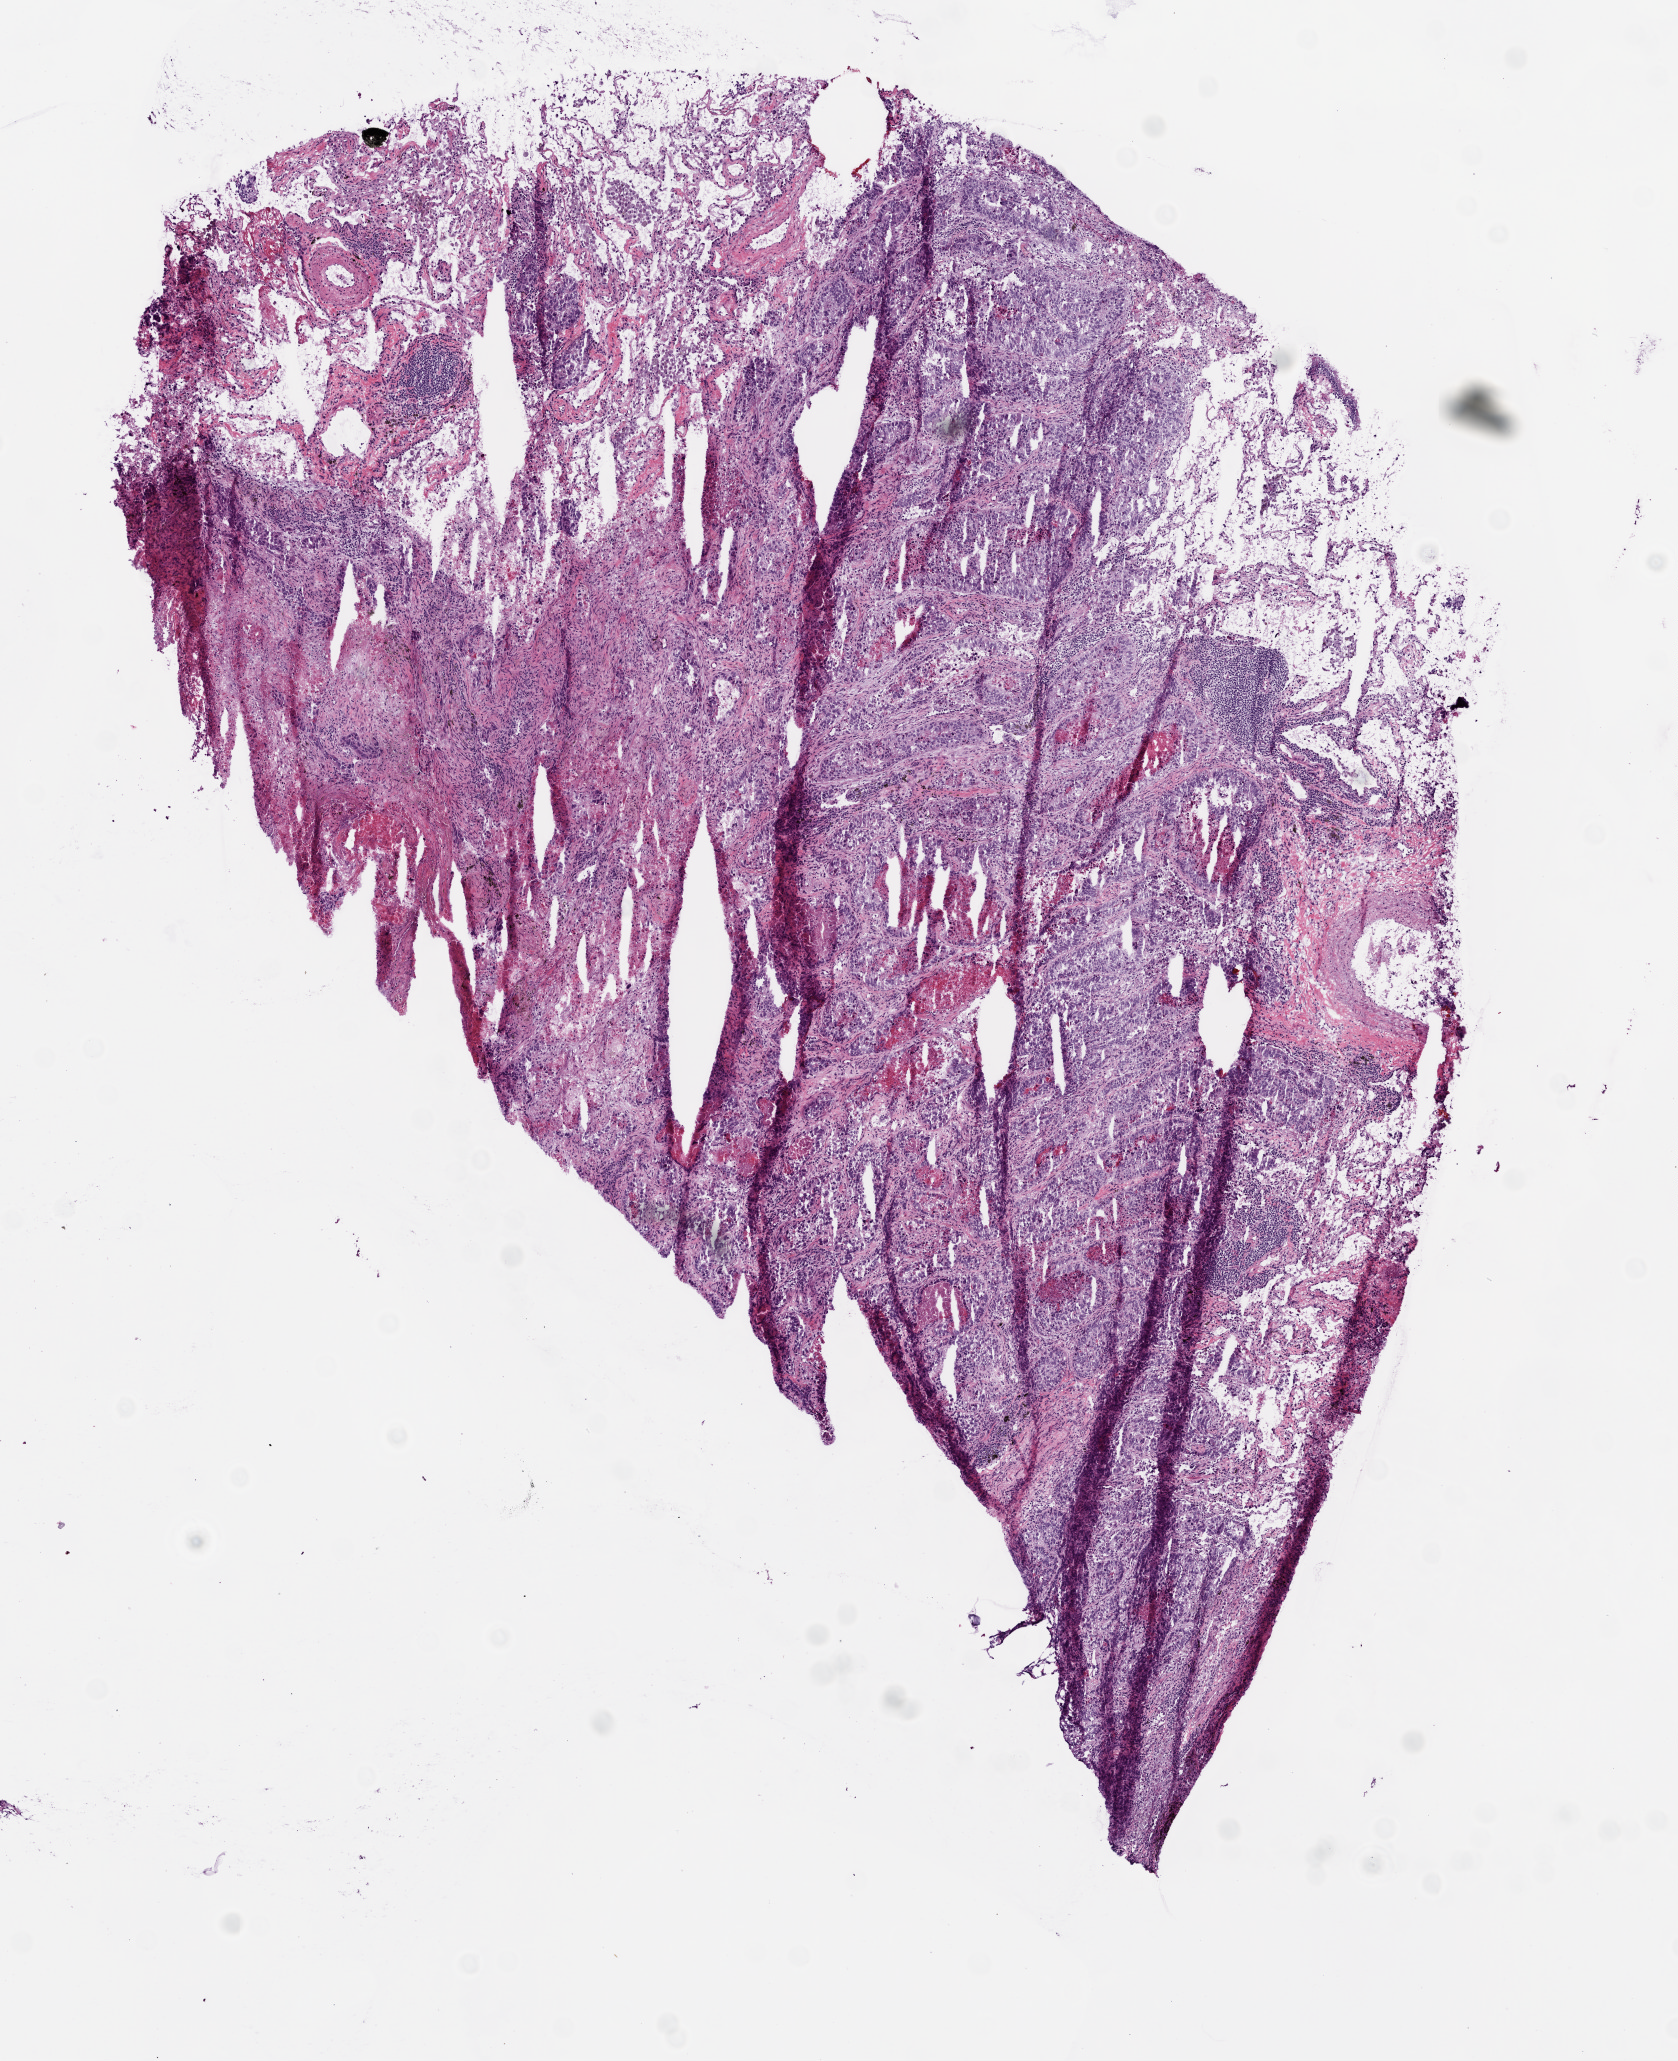
Whole-slide histology image, Hematoxylin and eosin (H&E) stained — low-resolution overview of the scanned area, about 6.8 x 8.3 mm (slide scanned at 20x), frozen section from the top of the tissue portion, lung, primary tumour sample. Female, age 47 years at initial diagnosis. Pathologist review of this section (percent, as recorded): tumour cells 90%, tumour nuclei 75%, normal cells 0%, stromal cells 0%, necrosis 10%. Inflammatory infiltration, as recorded: lymphocyte infiltration 20%, monocyte infiltration 5%.
Histologic diagnosis: Adenocarcinoma, NOS (upper lobe, lung). AJCC pathologic stage: IIA.